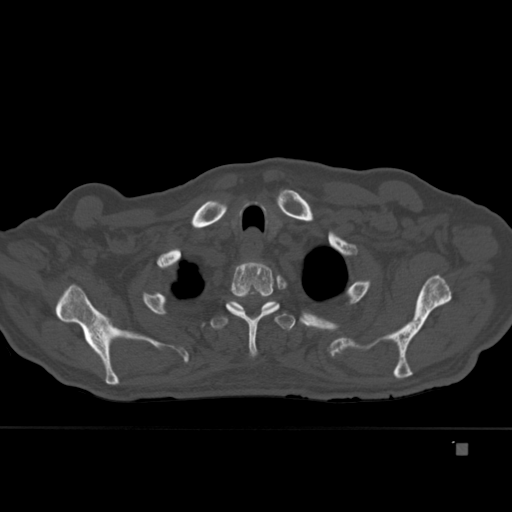
CT including the spine, one axial slice; slice 344 of 451 in the series (ordered by position); bone window (W 1800 / L 400 HU); 1.5 mm slice thickness; 512 × 512 image matrix, field of view 378 × 378 mm. Male patient, age 75 years. Case-level facts recorded for this patient, not image findings: primary cancer: prostate.
Structures marked on this image (semi-automatic segmentation, software-assisted and operator-edited):
- T2 vertebra: box from (x=226, y=262) to (x=280, y=357) px
- T3 vertebra: (x=210, y=300)–(x=296, y=331)